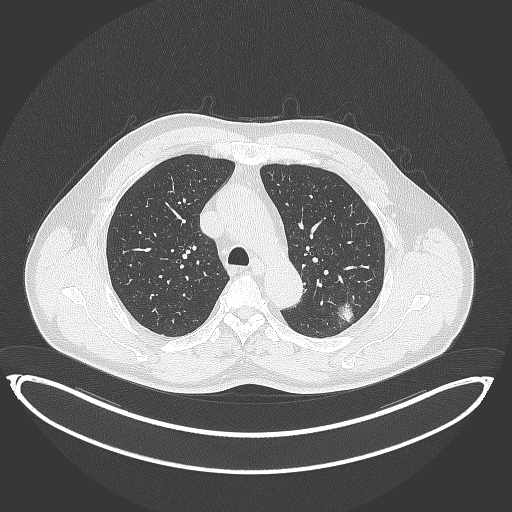
Chest CT, one axial slice; lung window (W 1500 / L -600 HU); 1 mm slice thickness; 512 × 512 image matrix, field of view 469 × 469 mm. Male patient, age 58 years. From the clinical record (not read from this slice): clinical TNM (as recorded): T1c N0 M0.
Annotated regions visible in this slice (bounding box drawn by a radiologist):
- lung tumour (recorded histology: adenocarcinoma): bounding box <333,296,361,329> (left, top, right, bottom; pixels)